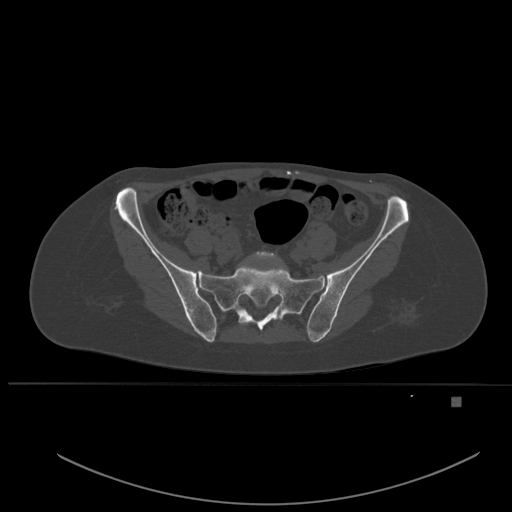
CT including the spine, one axial slice. Slice 137 of 651 in the series (ordered by position). Bone window (W 1800 / L 400 HU). 512 × 512 image matrix, field of view 443 × 443 mm. Female patient, age 49 years. Case-level facts recorded for this patient, not image findings: primary cancer: breast.
Outlined on this slice (semi-automatically segmented with operator editing):
- L5 vertebra: box from (x=254, y=251) to (x=291, y=278) px